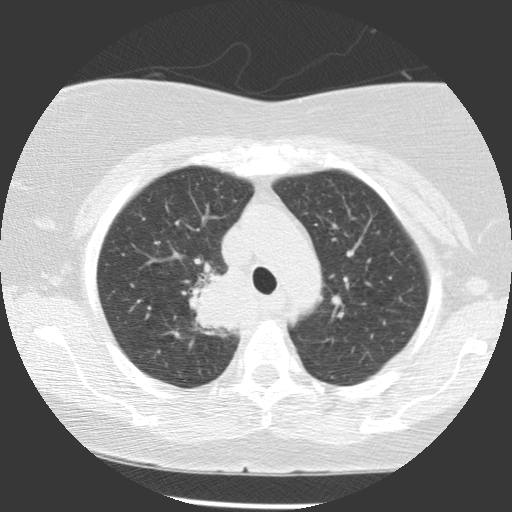
Low-dose screening chest CT, axial slice. Baseline screening round. Lung window (W 1500 / L -600 HU). 2.5 mm slice thickness. Standard (soft-tissue) reconstruction kernel (STANDARD). 140 kVp. 512 × 512 image matrix. Female, age 63 years at enrolment. Former smoker at enrolment.
- Expert-annotated lung lesion, bounding box (x1, y1, x2, y2) in pixels: (195, 265, 255, 326).
- Reader record for this screening exam (exam-level; its link to the box is not recorded): non-calcified nodule or mass ≥4 mm, right upper lobe, 39 × 36 mm, spiculated (stellate) margins, soft tissue attenuation.
- Official screen result: positive, change unspecified: nodule(s) >= 4 mm or enlarging nodule(s), mass(es), or other non-specific abnormalities suspicious for lung cancer.
- Participant outcome: lung cancer diagnosed 72 days after this screen — non-small cell carcinoma, right upper lobe, carina, right main stem bronchus, poorly differentiated (G3), stage IIIA (AJCC 6th edition), 66 mm at pathology.